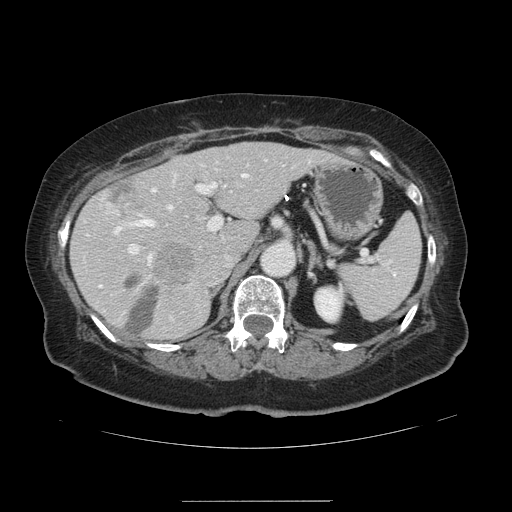
Contrast-enhanced abdominal CT, one axial slice; slice 82 of 141 in the series (ordered by position); 120 kVp; intravenous contrast given; soft-tissue window (W 400 / L 40 HU); 512 × 512 image matrix, field of view 393 × 393 mm. Female patient, age 74 years. From the clinical record (not read from this slice): diagnosis: colorectal cancer liver metastases, imaged before liver resection; multiple liver metastases: yes; largest metastasis: 7 cm; disease in both lobes: yes.
Outlined on this slice (expert manual segmentation):
- hepatic veins: bounding box (x1, y1, x2, y2) in pixels: (115, 173, 246, 232)
- liver: (72, 143, 329, 342)
- planned liver remnant (the part of the liver to remain after resection): (72, 143, 329, 341)
- portal vein (with intrahepatic branches): (128, 159, 265, 262)
- liver metastasis: (103, 176, 141, 216)
- liver metastasis: (127, 276, 160, 335)
- liver metastasis: (156, 242, 195, 286)